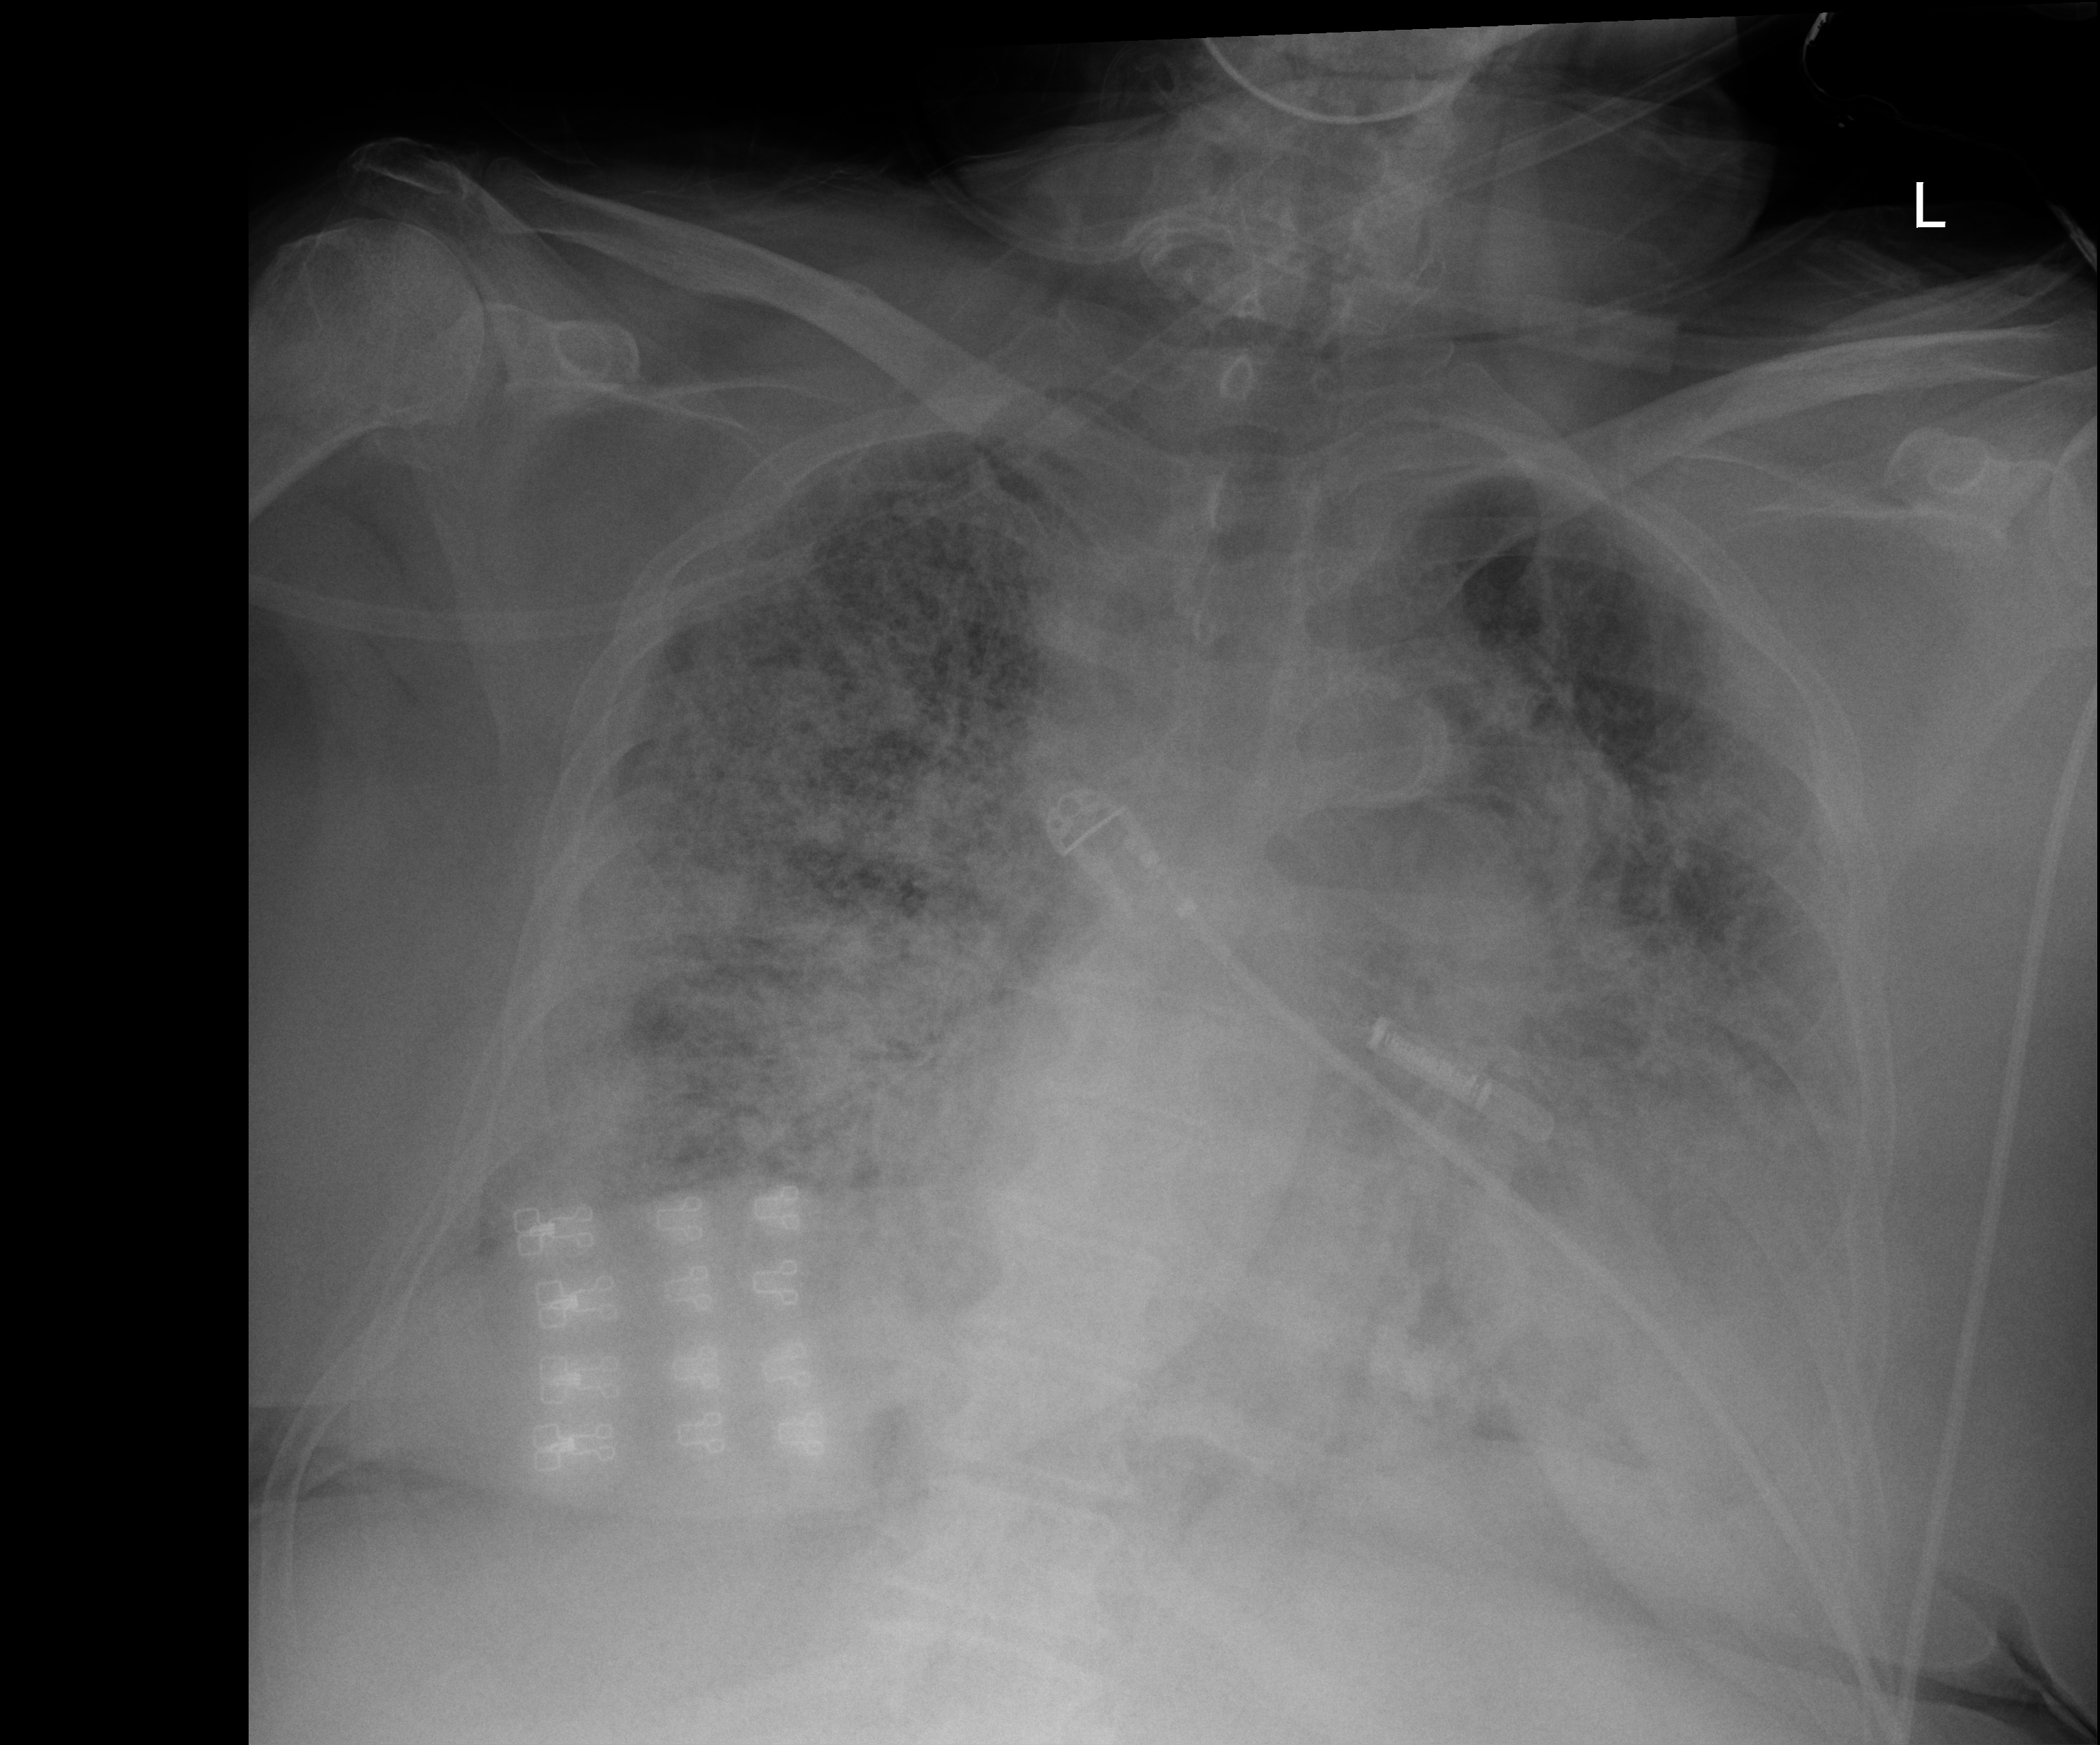
Bedside chest radiograph (digital radiography); anteroposterior (AP) projection. Patient hospitalised with COVID-19; female, aged 60–74 years.
Hospital-stay facts (about this admission, not read from this image; timing relative to this image not recorded): admitted to intensive care during this hospital stay: yes; length of hospital stay: 28 days.